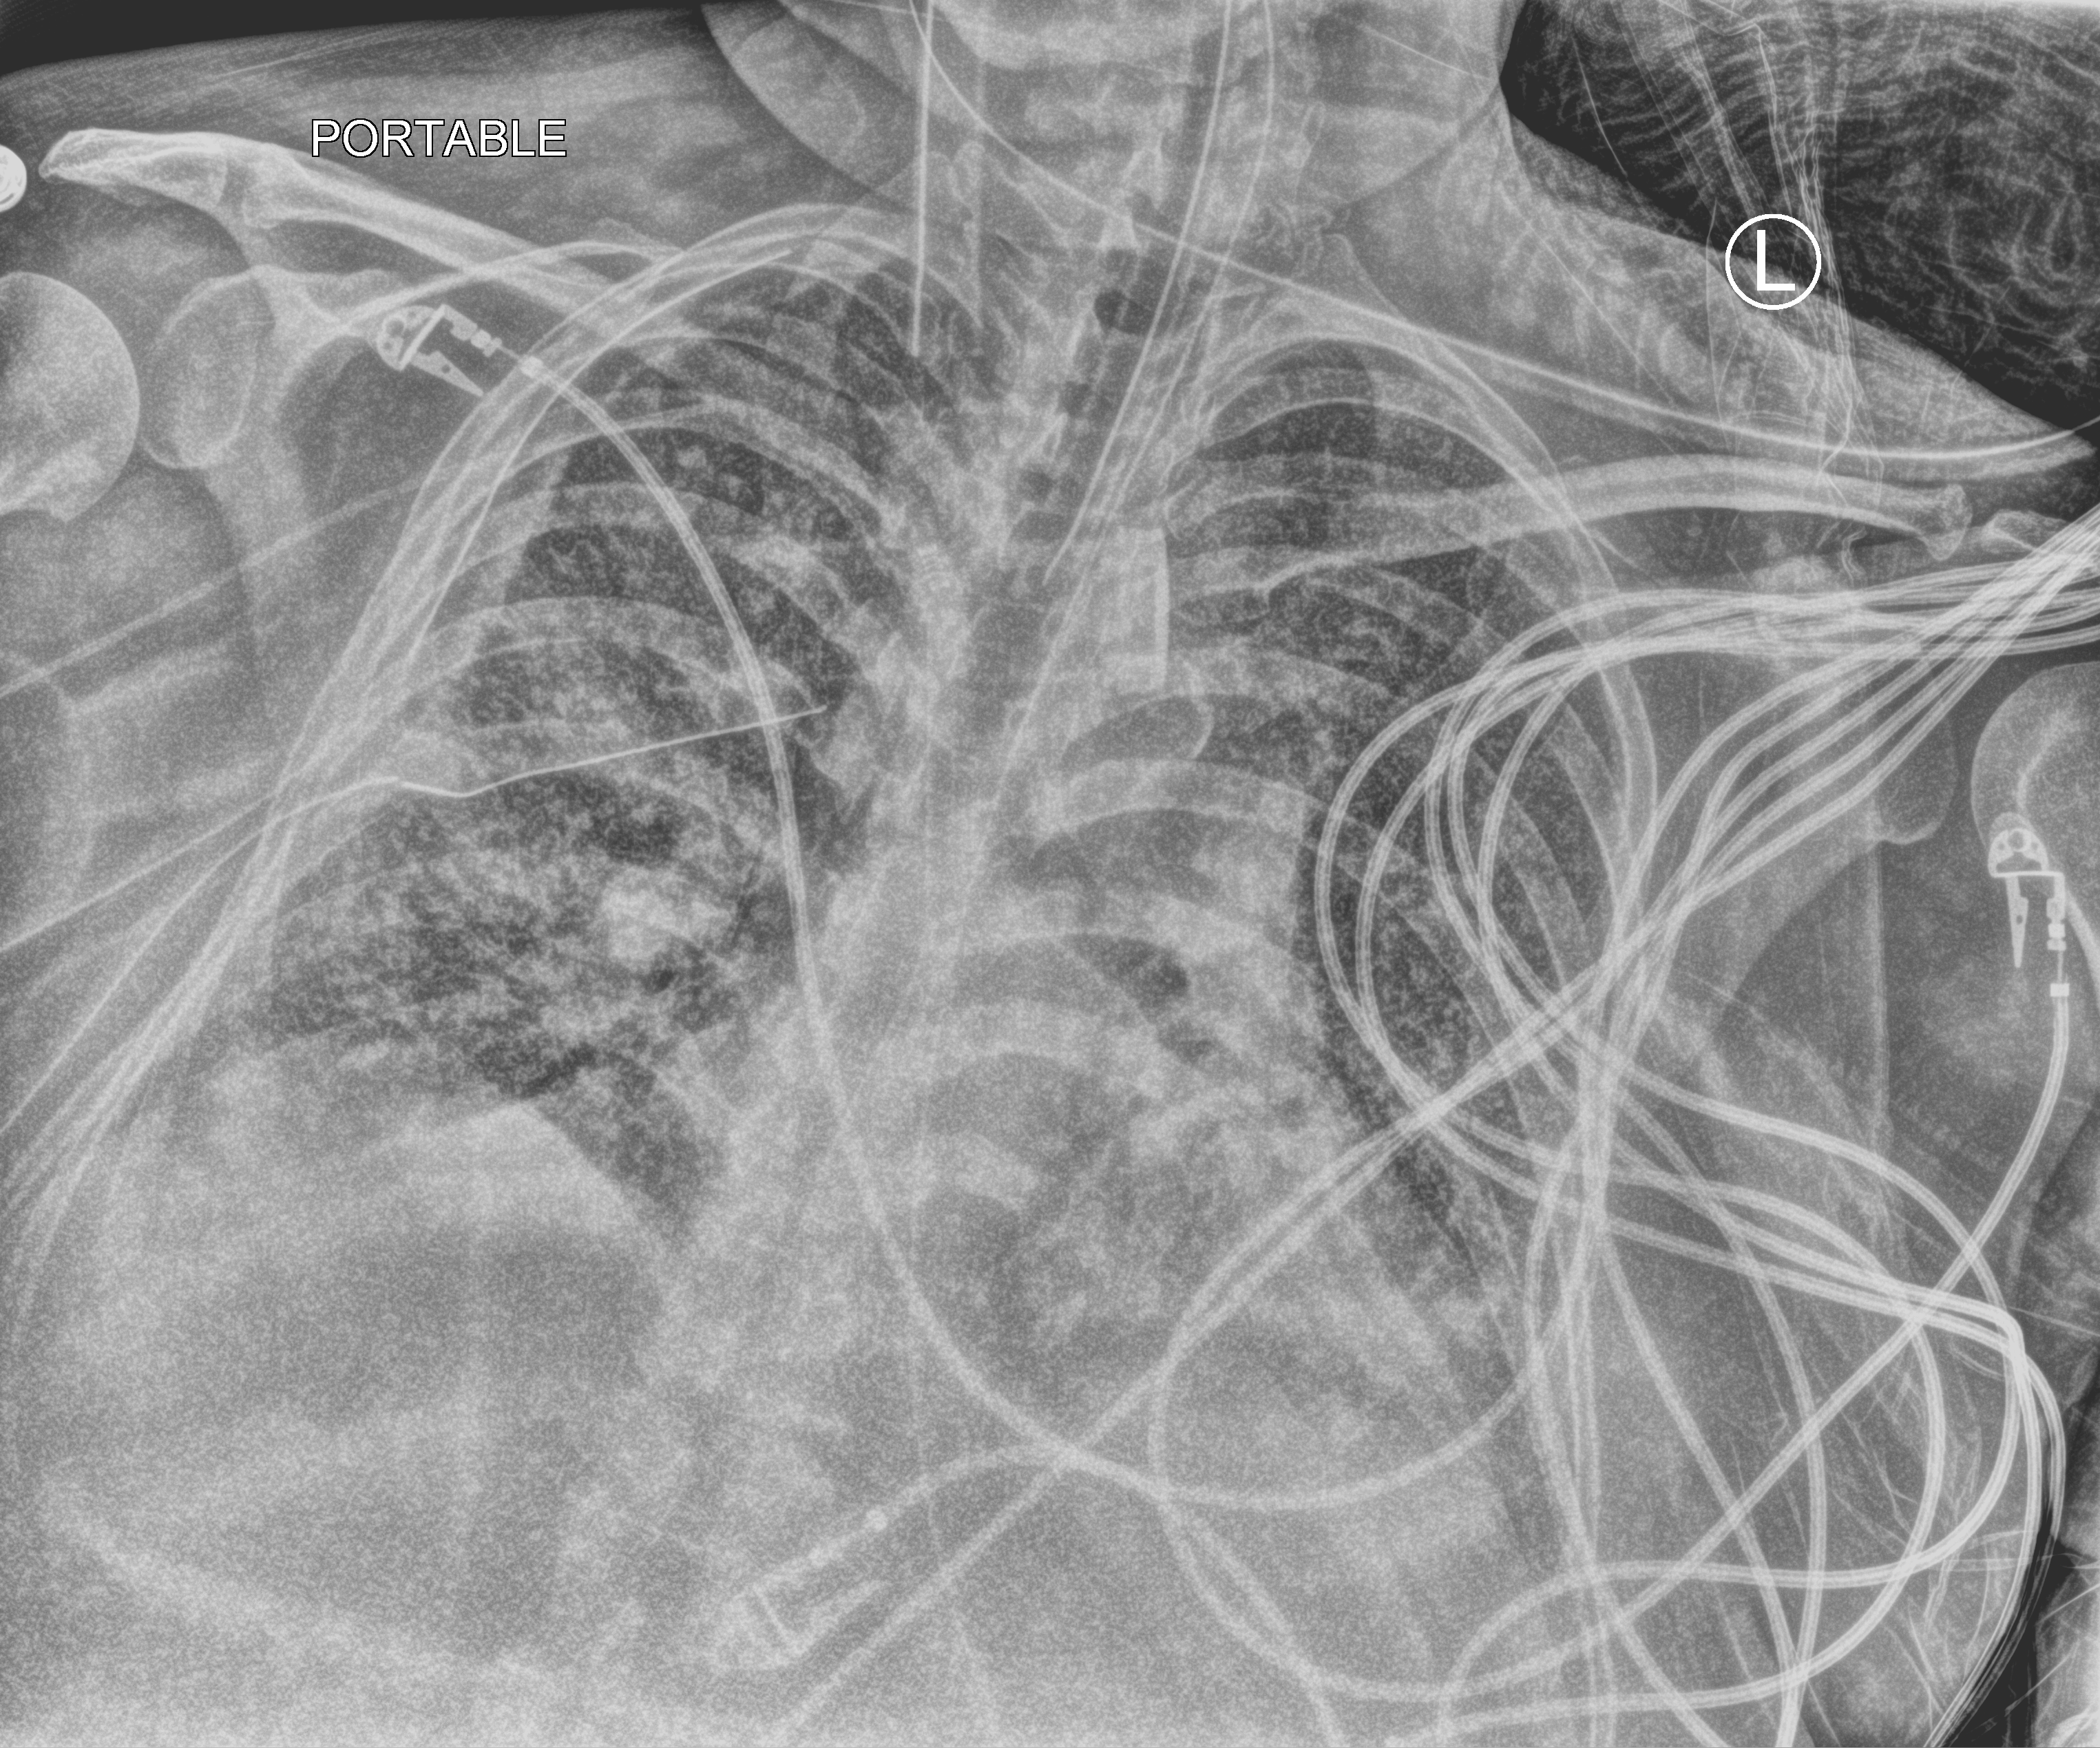
Portable chest radiograph, anteroposterior (AP) projection. Adult patient hospitalised with COVID-19, age 18–59 years.
Admission-level facts for this patient (not findings on this image; timing relative to this image not recorded):
- admitted to intensive care during this hospital stay: yes
- mechanically ventilated during this hospital stay: yes